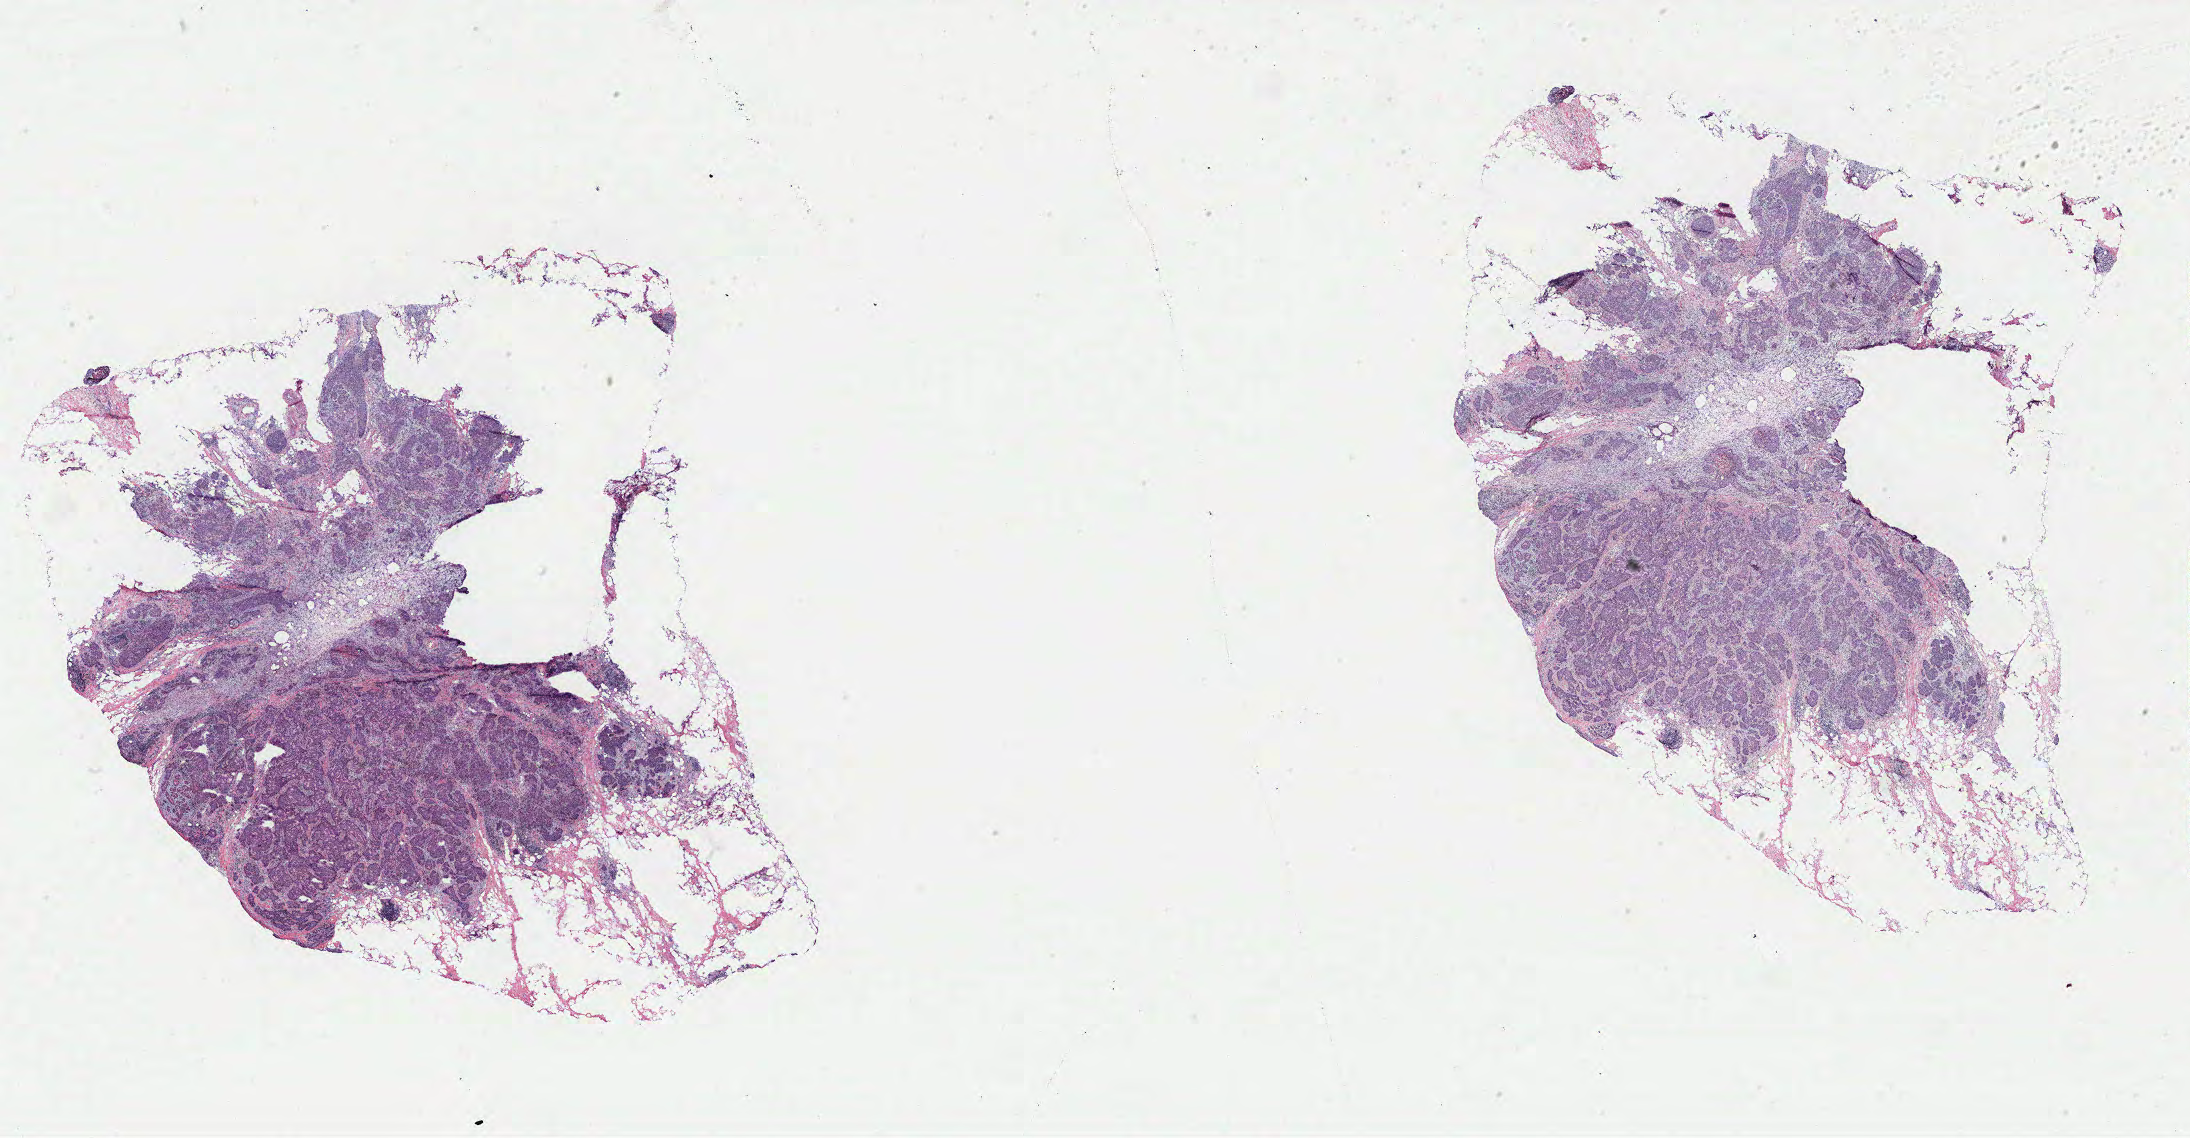
Whole-slide histology image, H&E-stained — low-resolution overview of the scanned area, about 35.1 x 18.2 mm (acquisition: 40x scan). Breast, tumour tissue. Female, 37 y/o.
AJCC pathologic stage: IIA. Histologic diagnosis: Infiltrating duct carcinoma, NOS.